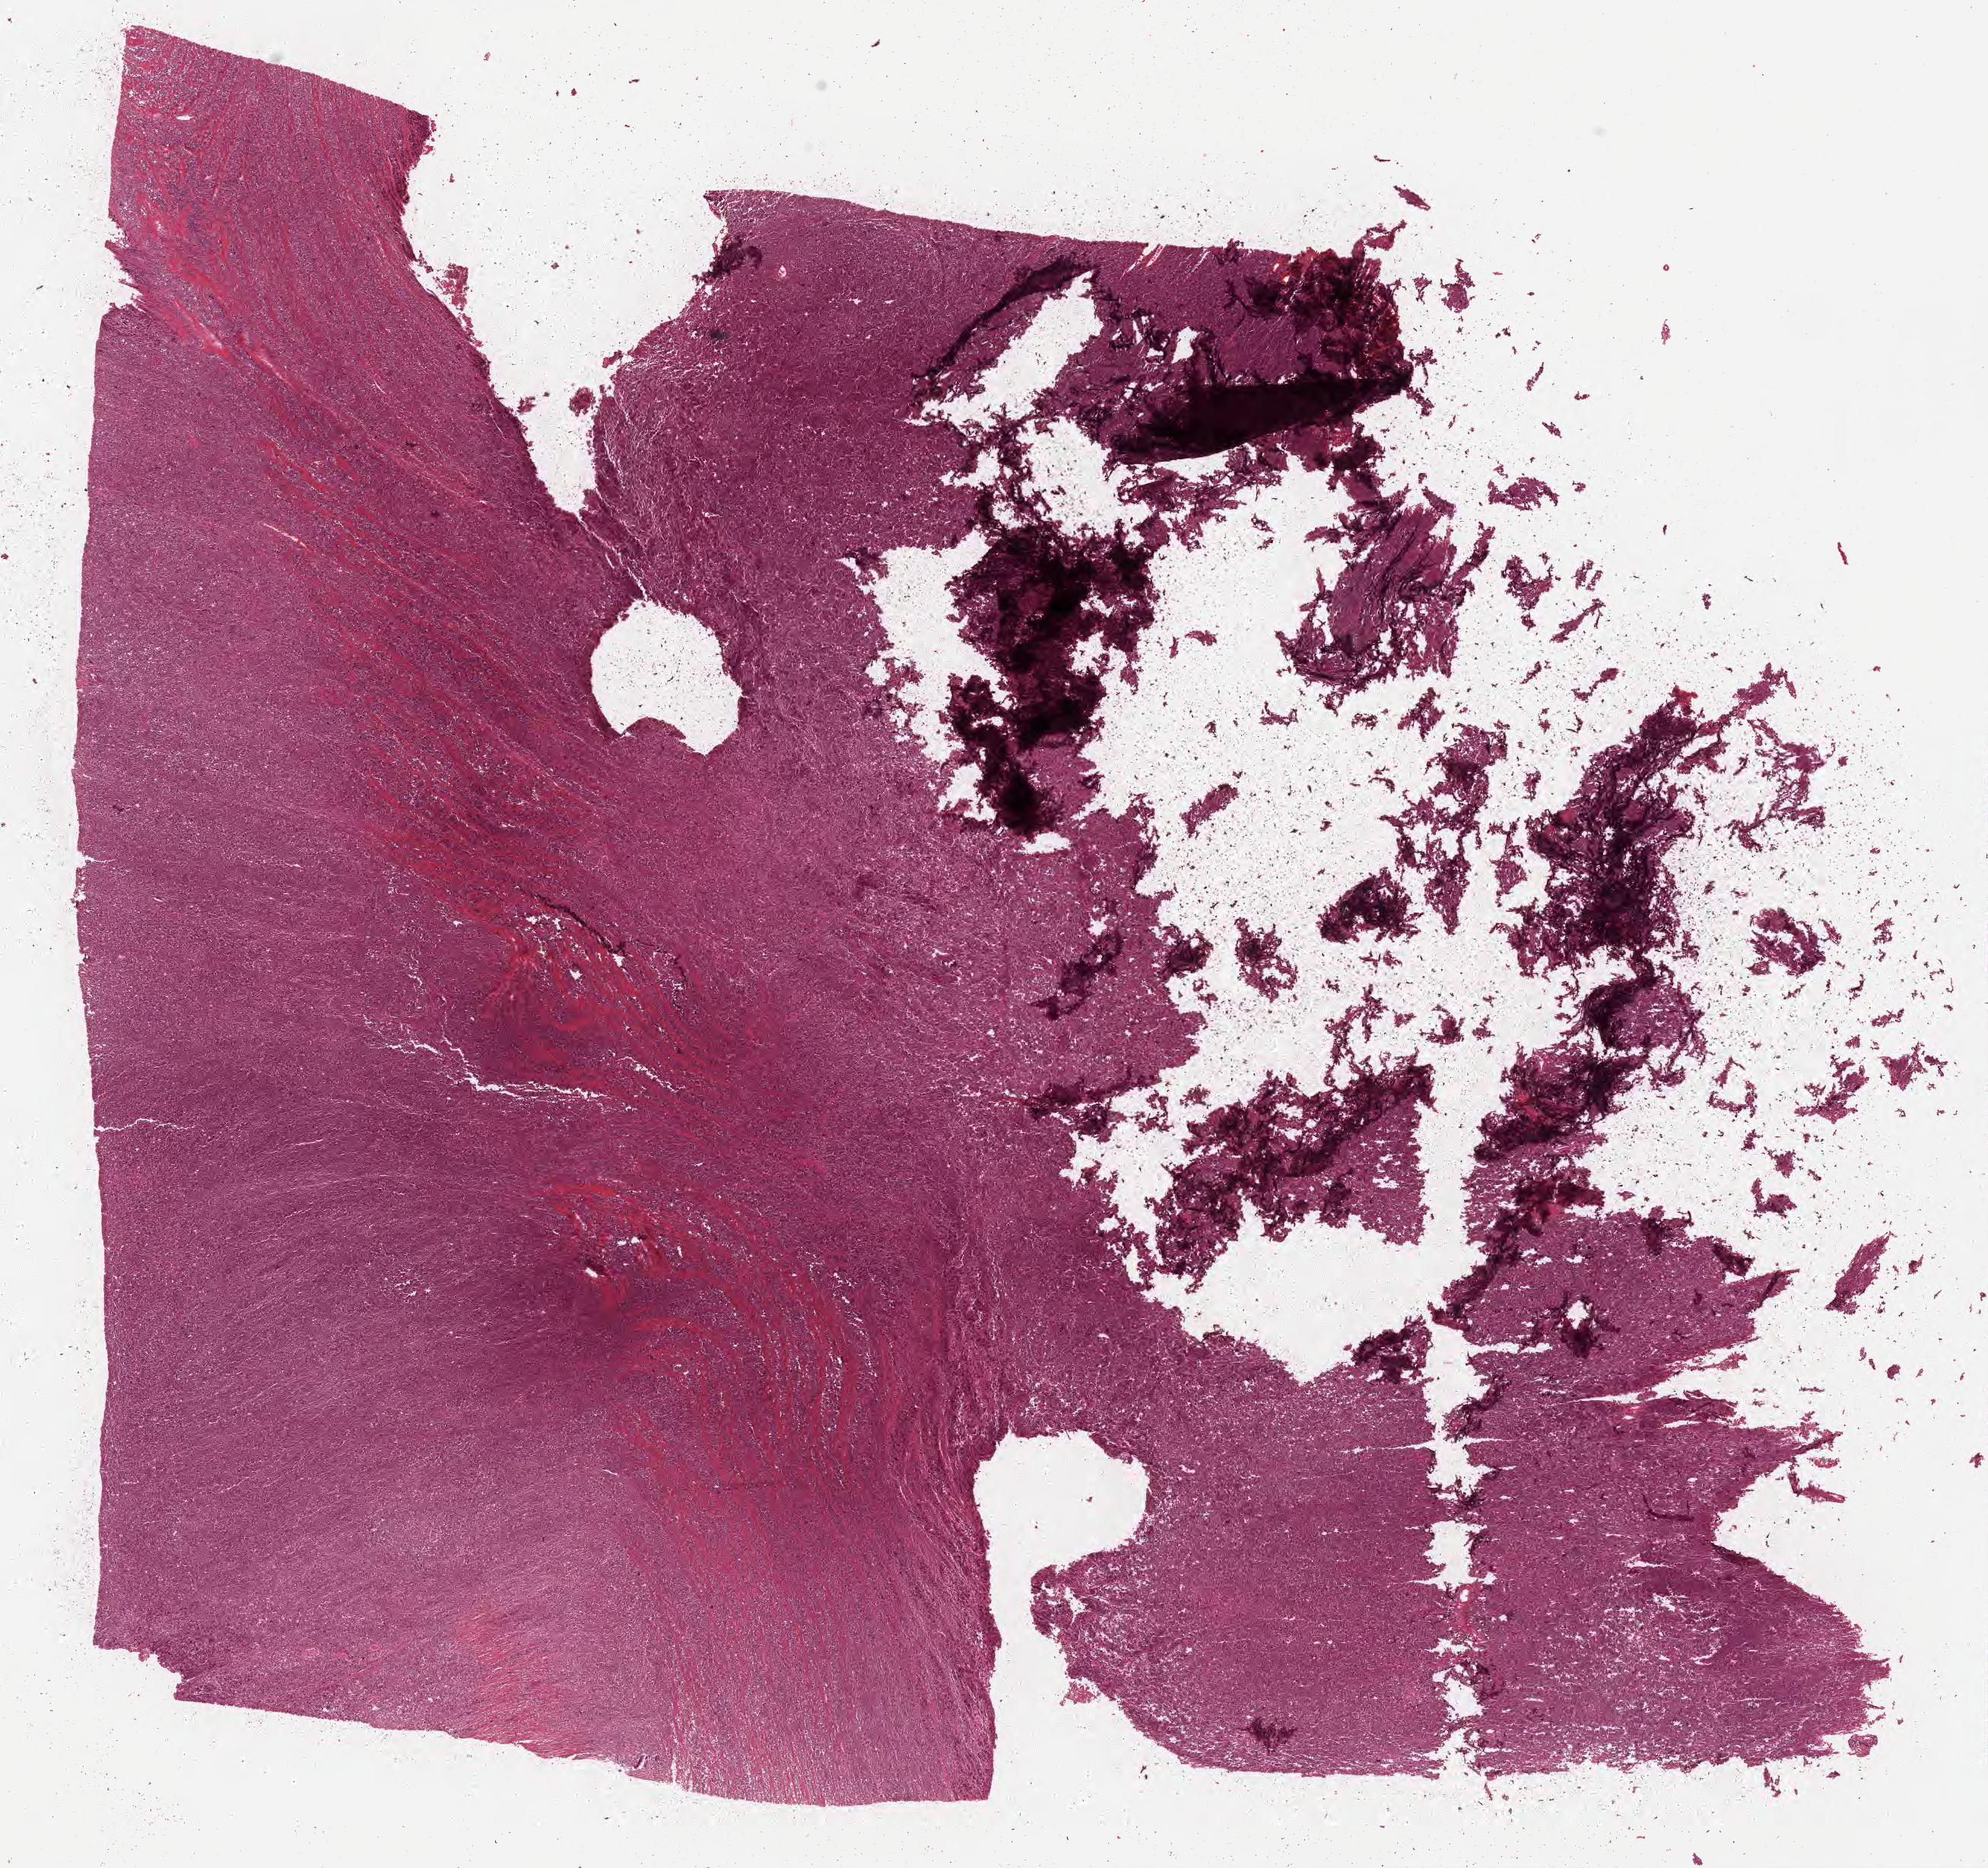
Whole-slide image, hematoxylin and eosin (H&E) stain, shown as a low-resolution overview of the whole scanned area (about 21.1 x 19.9 mm), formalin-fixed, paraffin-embedded (FFPE) tissue, specimen: primary tumor. Patient male; age 17 years. Slide review estimates, as recorded: tumor cells 90%, tumor nuclei 95%, stromal cells 5%, necrosis 5%, normal cells 0%. Infiltration values recorded for this section: lymphocyte infiltration 80%, monocyte infiltration 10%, neutrophil infiltration 0%.
Ann Arbor stage (patient): Stage III. Diagnosis: Burkitt lymphoma, NOS.